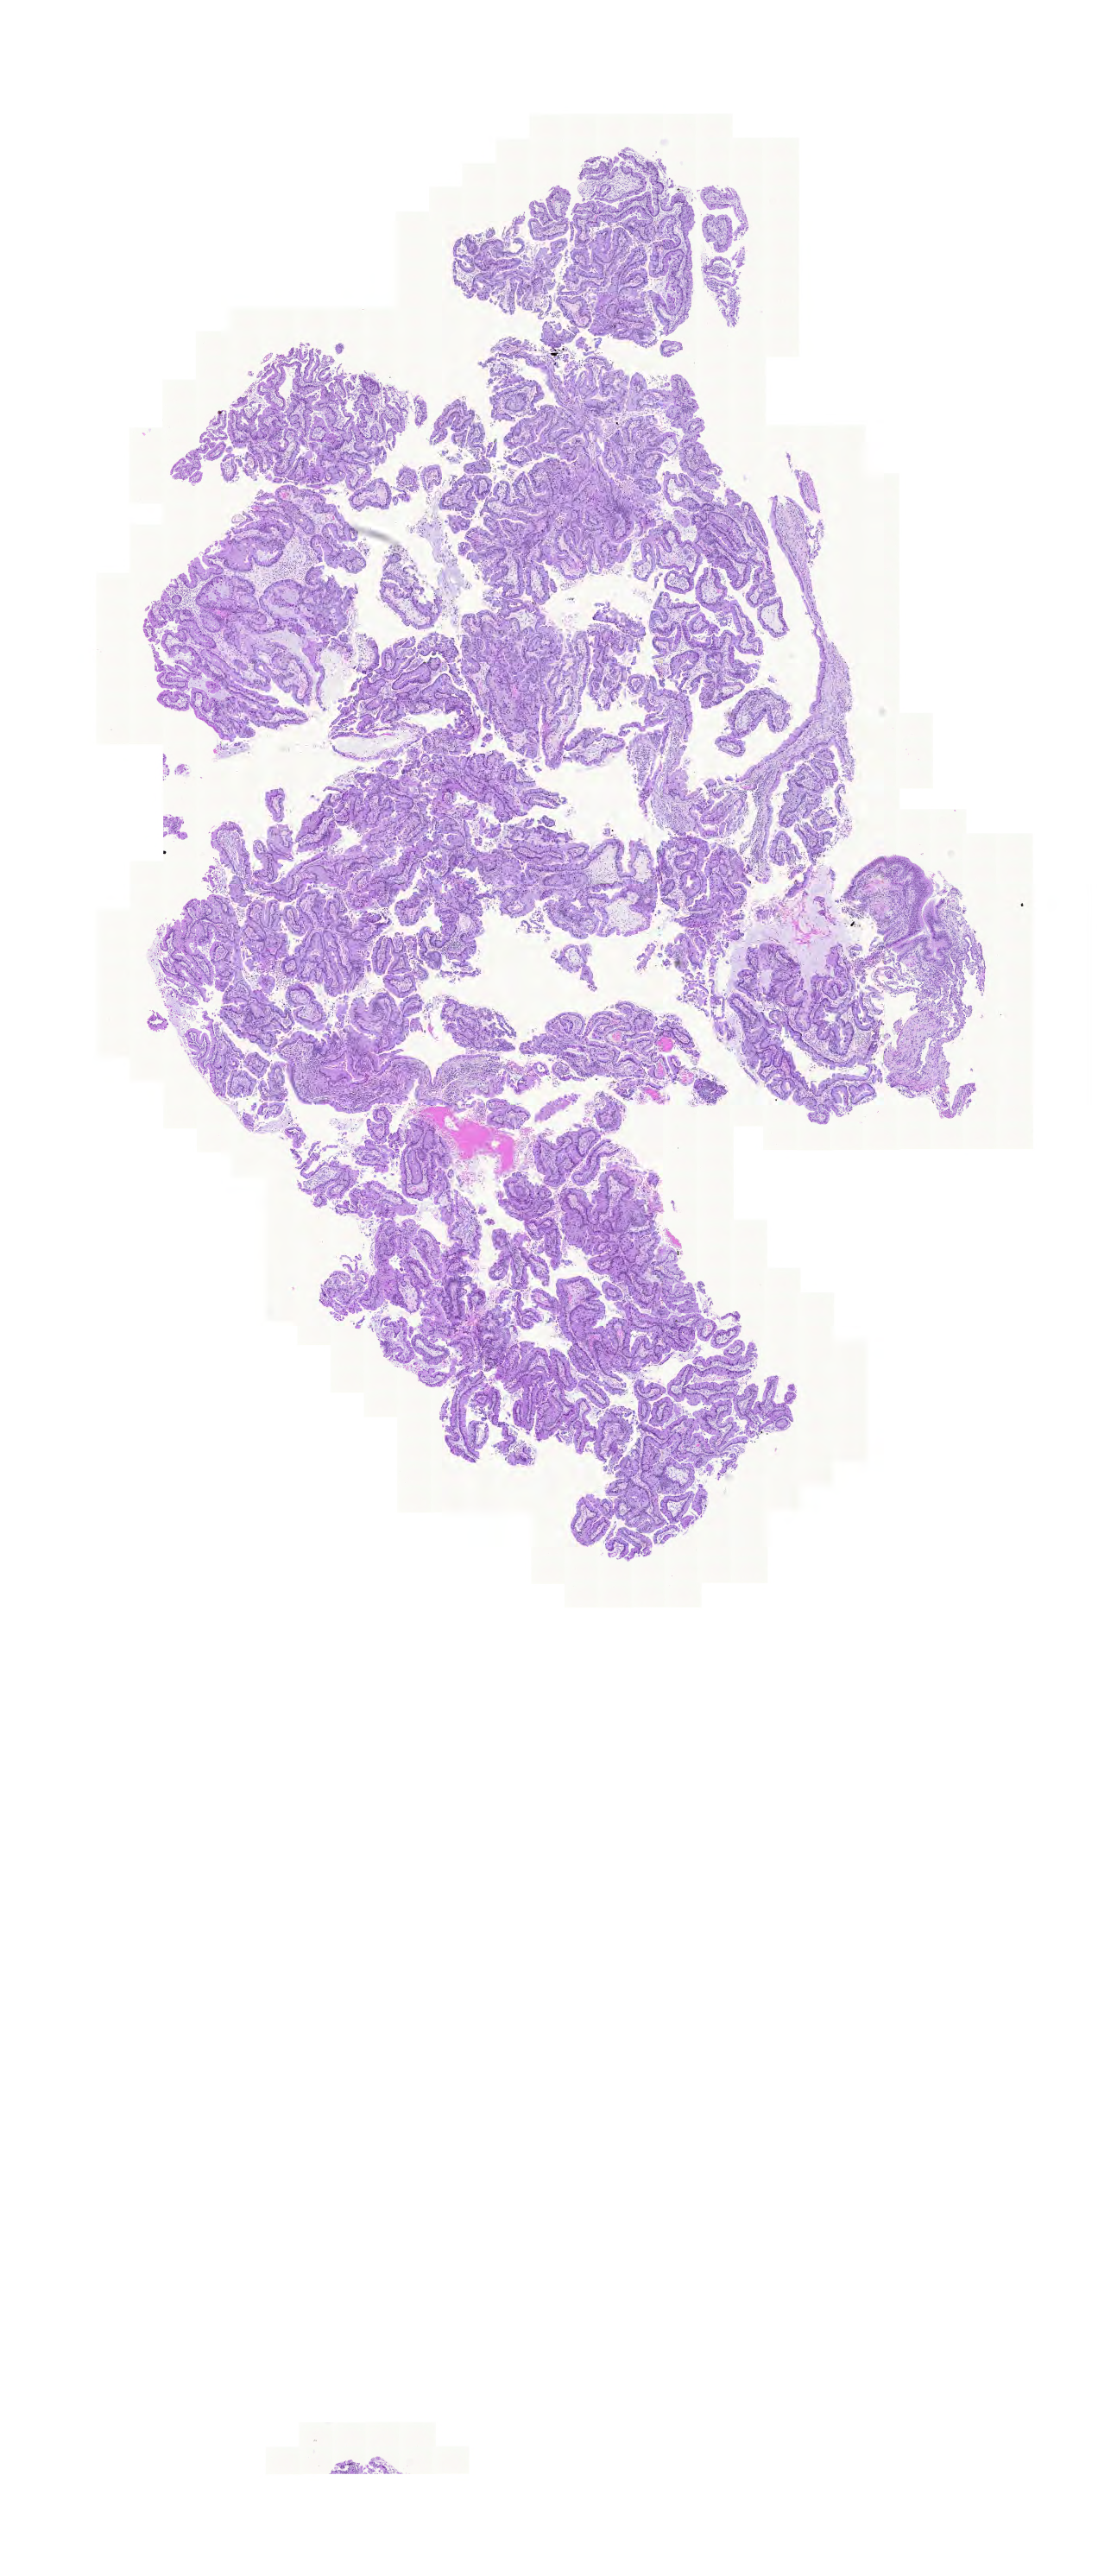
Digitized H&E tissue section (whole slide) — low-resolution overview of the scanned area, about 9.5 x 22.2 mm (acquisition: 20x scan). FFPE section. Primary tumour sample from the lung. Male patient; age at initial diagnosis 41 years.
Pathologic diagnosis: Adenocarcinoma with mixed subtypes (lower lobe, lung).